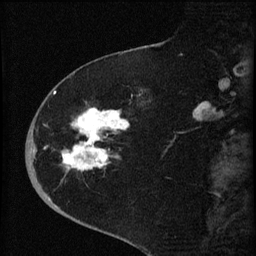
Breast MRI (dynamic contrast-enhanced), one sagittal slice; position 24 of 60 along the scan axis; dynamic contrast-enhanced series, image 2 of 4 at this slice position (ordered by acquisition); 1.5 T; TE 4.2 ms, TR 8.2 ms; 2 mm slice thickness; 256 × 256 image matrix, field of view 180 × 180 mm. Female patient, age 71 years.
Annotated regions visible in this slice (semi-automatic segmentation, software-assisted and operator-edited):
- analysis volume of interest (the breast-tissue region the enhancement analysis was run in; not a lesion): bounding box [x1, y1, x2, y2] px = [35, 75, 147, 190]
- tumour enhancement mask (voxels above the 70 % enhancement threshold inside the analysis volume of interest): [45, 92, 129, 171]